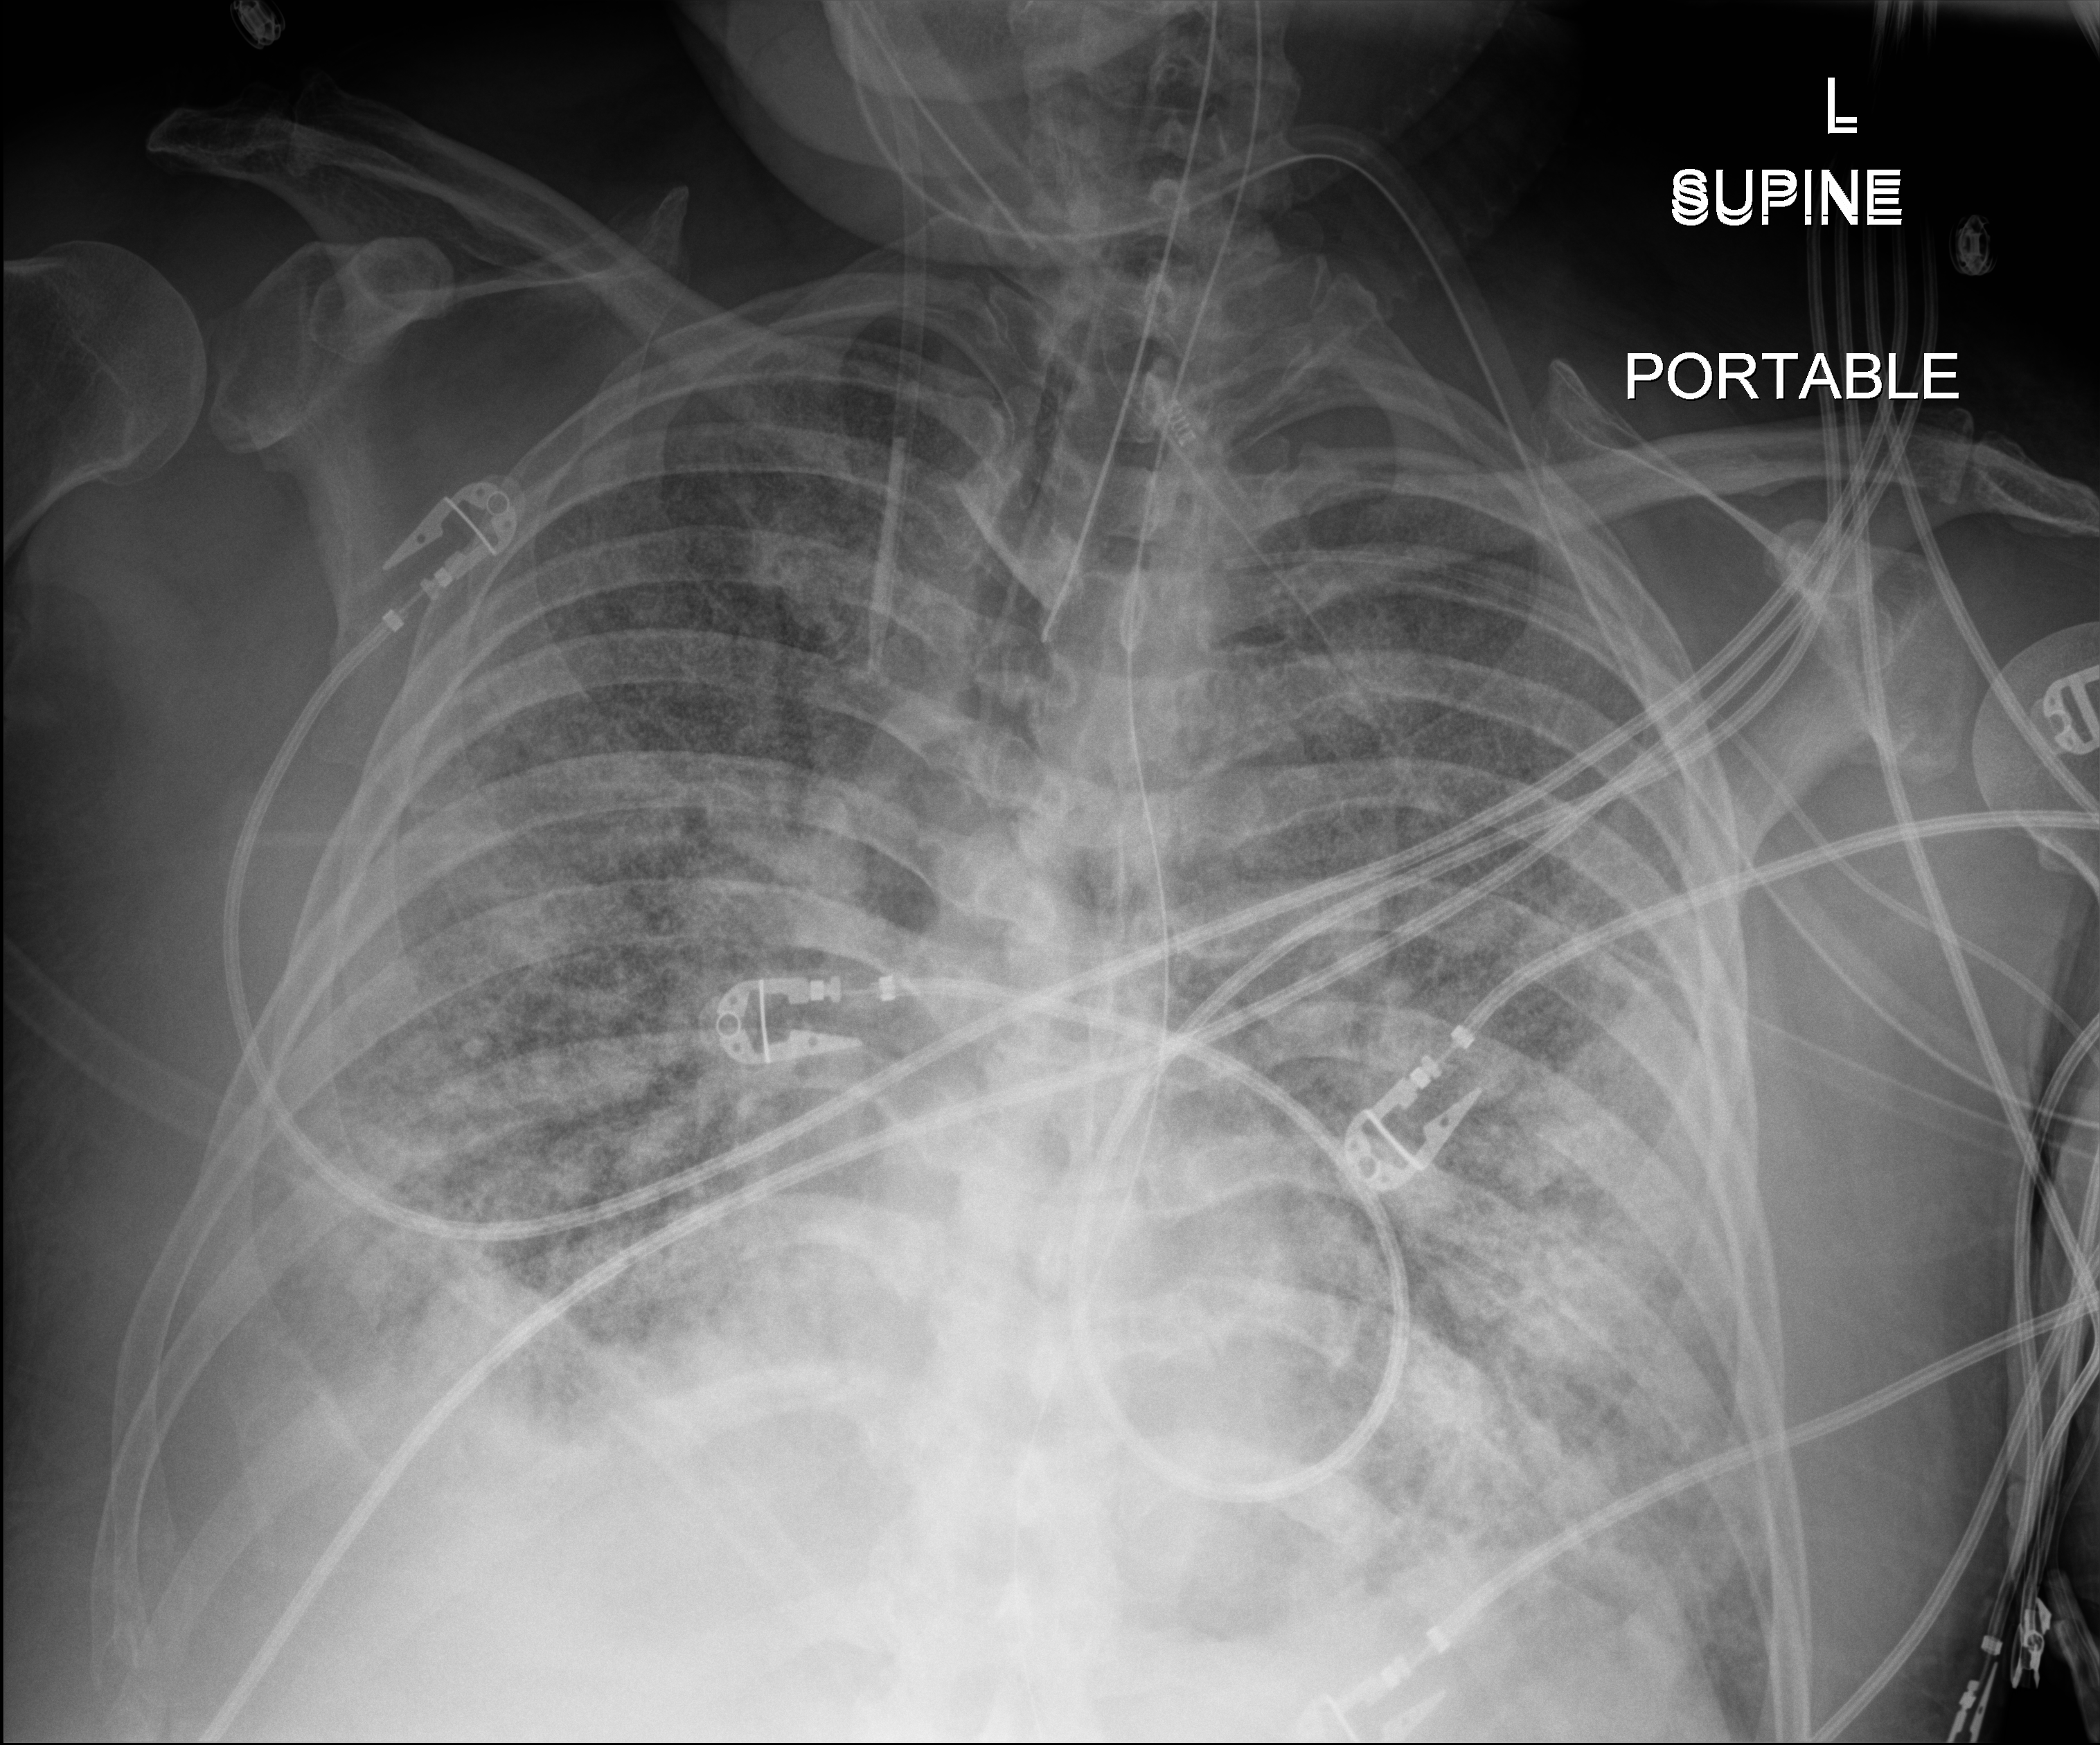
Portable chest radiograph; anteroposterior (AP) projection. Male patient hospitalised with COVID-19, age 60–74 years.
Admission-level facts for this patient (not findings on this image; timing relative to this image not recorded):
- other chronic lung disease (admission record): no